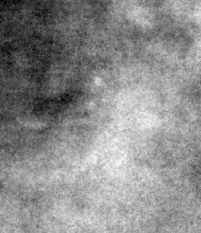
Crop from a digitized film mammogram around one marked abnormality; right breast; CC view.
- Marked abnormality: calcifications, morphology amorphous / pleomorphic, distribution clustered; BI-RADS assessment category 4; subtlety rating 2 on a 1 (subtle) to 5 (obvious) scale; pathology result (as recorded, not read from the image): benign.